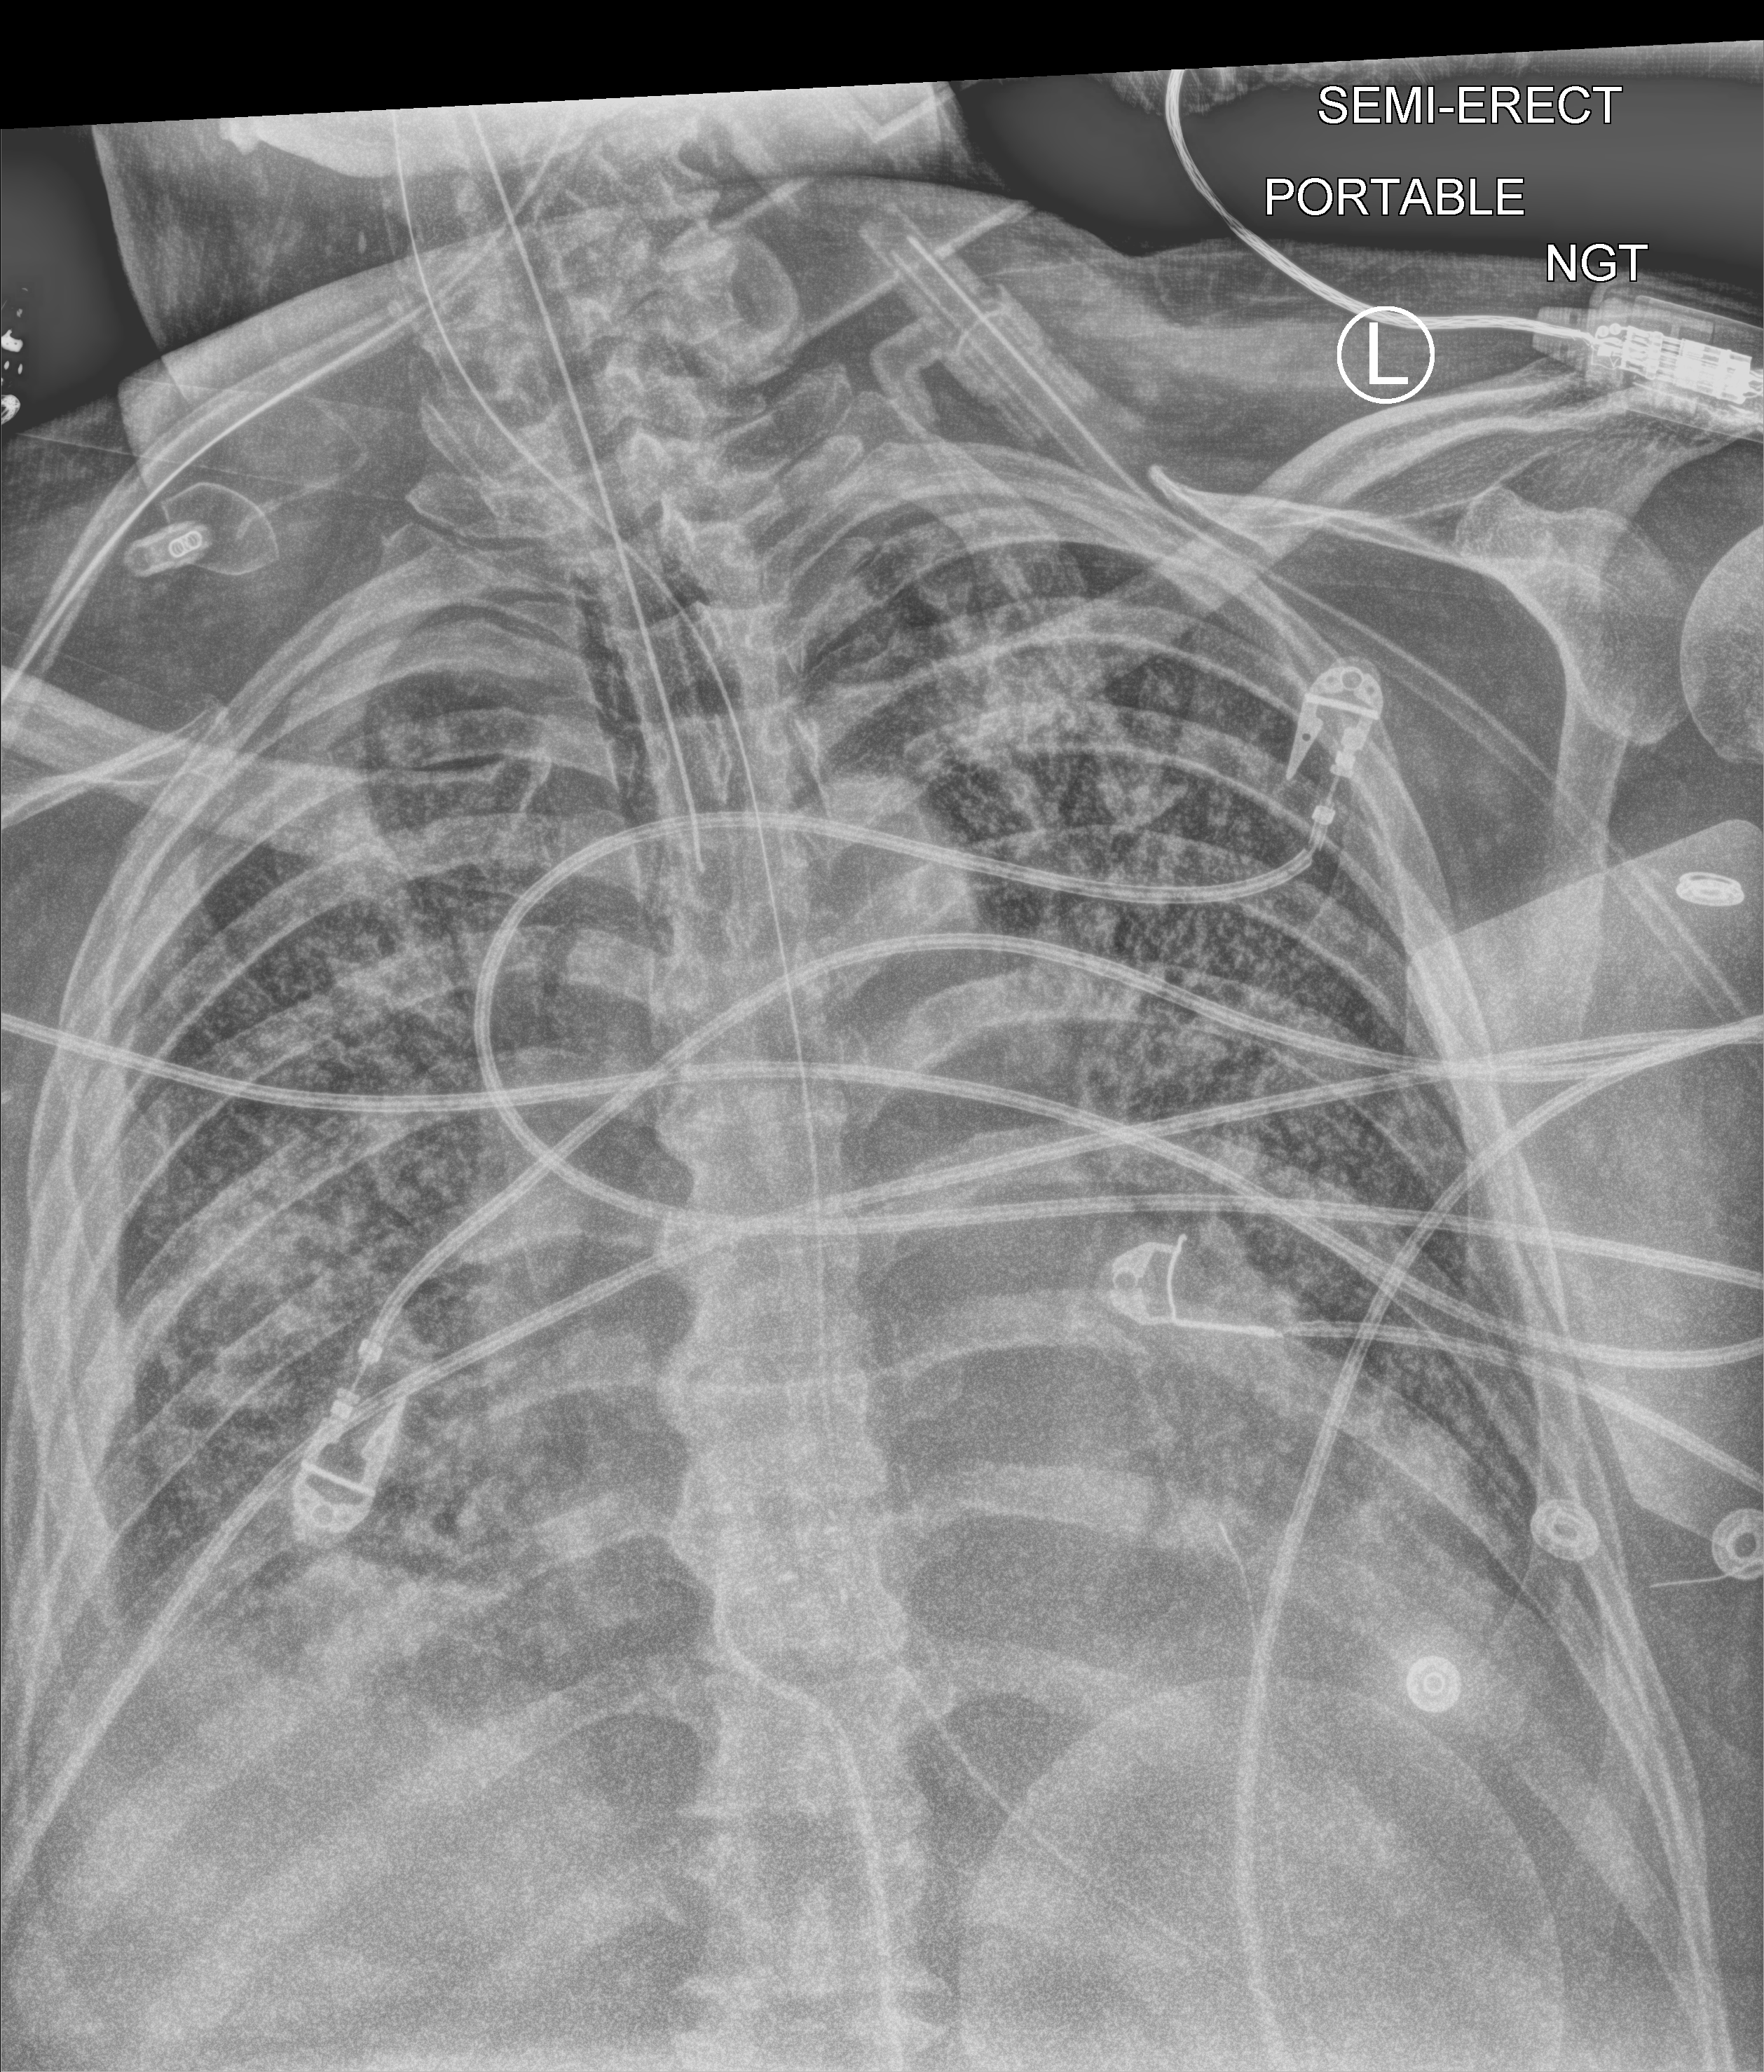
Bedside chest radiograph (computed radiography); anteroposterior (AP) projection. Male patient hospitalised with COVID-19, age 60–74 years.
Admission-level facts for this patient (not findings on this image; timing relative to this image not recorded): chronic kidney disease (admission record): no; mechanically ventilated during this hospital stay: yes; admitted to intensive care during this hospital stay: yes.